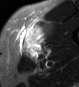
MRI of an extremity soft-tissue mass, one axial slice. Position 31 of 45 along the scan axis. STIR. MR volume resampled by the dataset authors to the PET/CT grid (not the native acquisition matrix). 79 × 87 image matrix, field of view 77 × 85 mm. Male patient. Case-level facts recorded for this patient, not image findings: histological type: pleiomorphic leiomyosarcoma; grade: high; site of the primary tumour: left thigh.
Annotated regions visible in this slice (expert contour drawn on MRI and transferred to this co-registered scan by the dataset authors):
- gross tumour volume including surrounding oedema: bounding box (x1, y1, x2, y2) in pixels: (20, 23, 51, 60)
- gross tumour volume (mass): (24, 29, 44, 58)